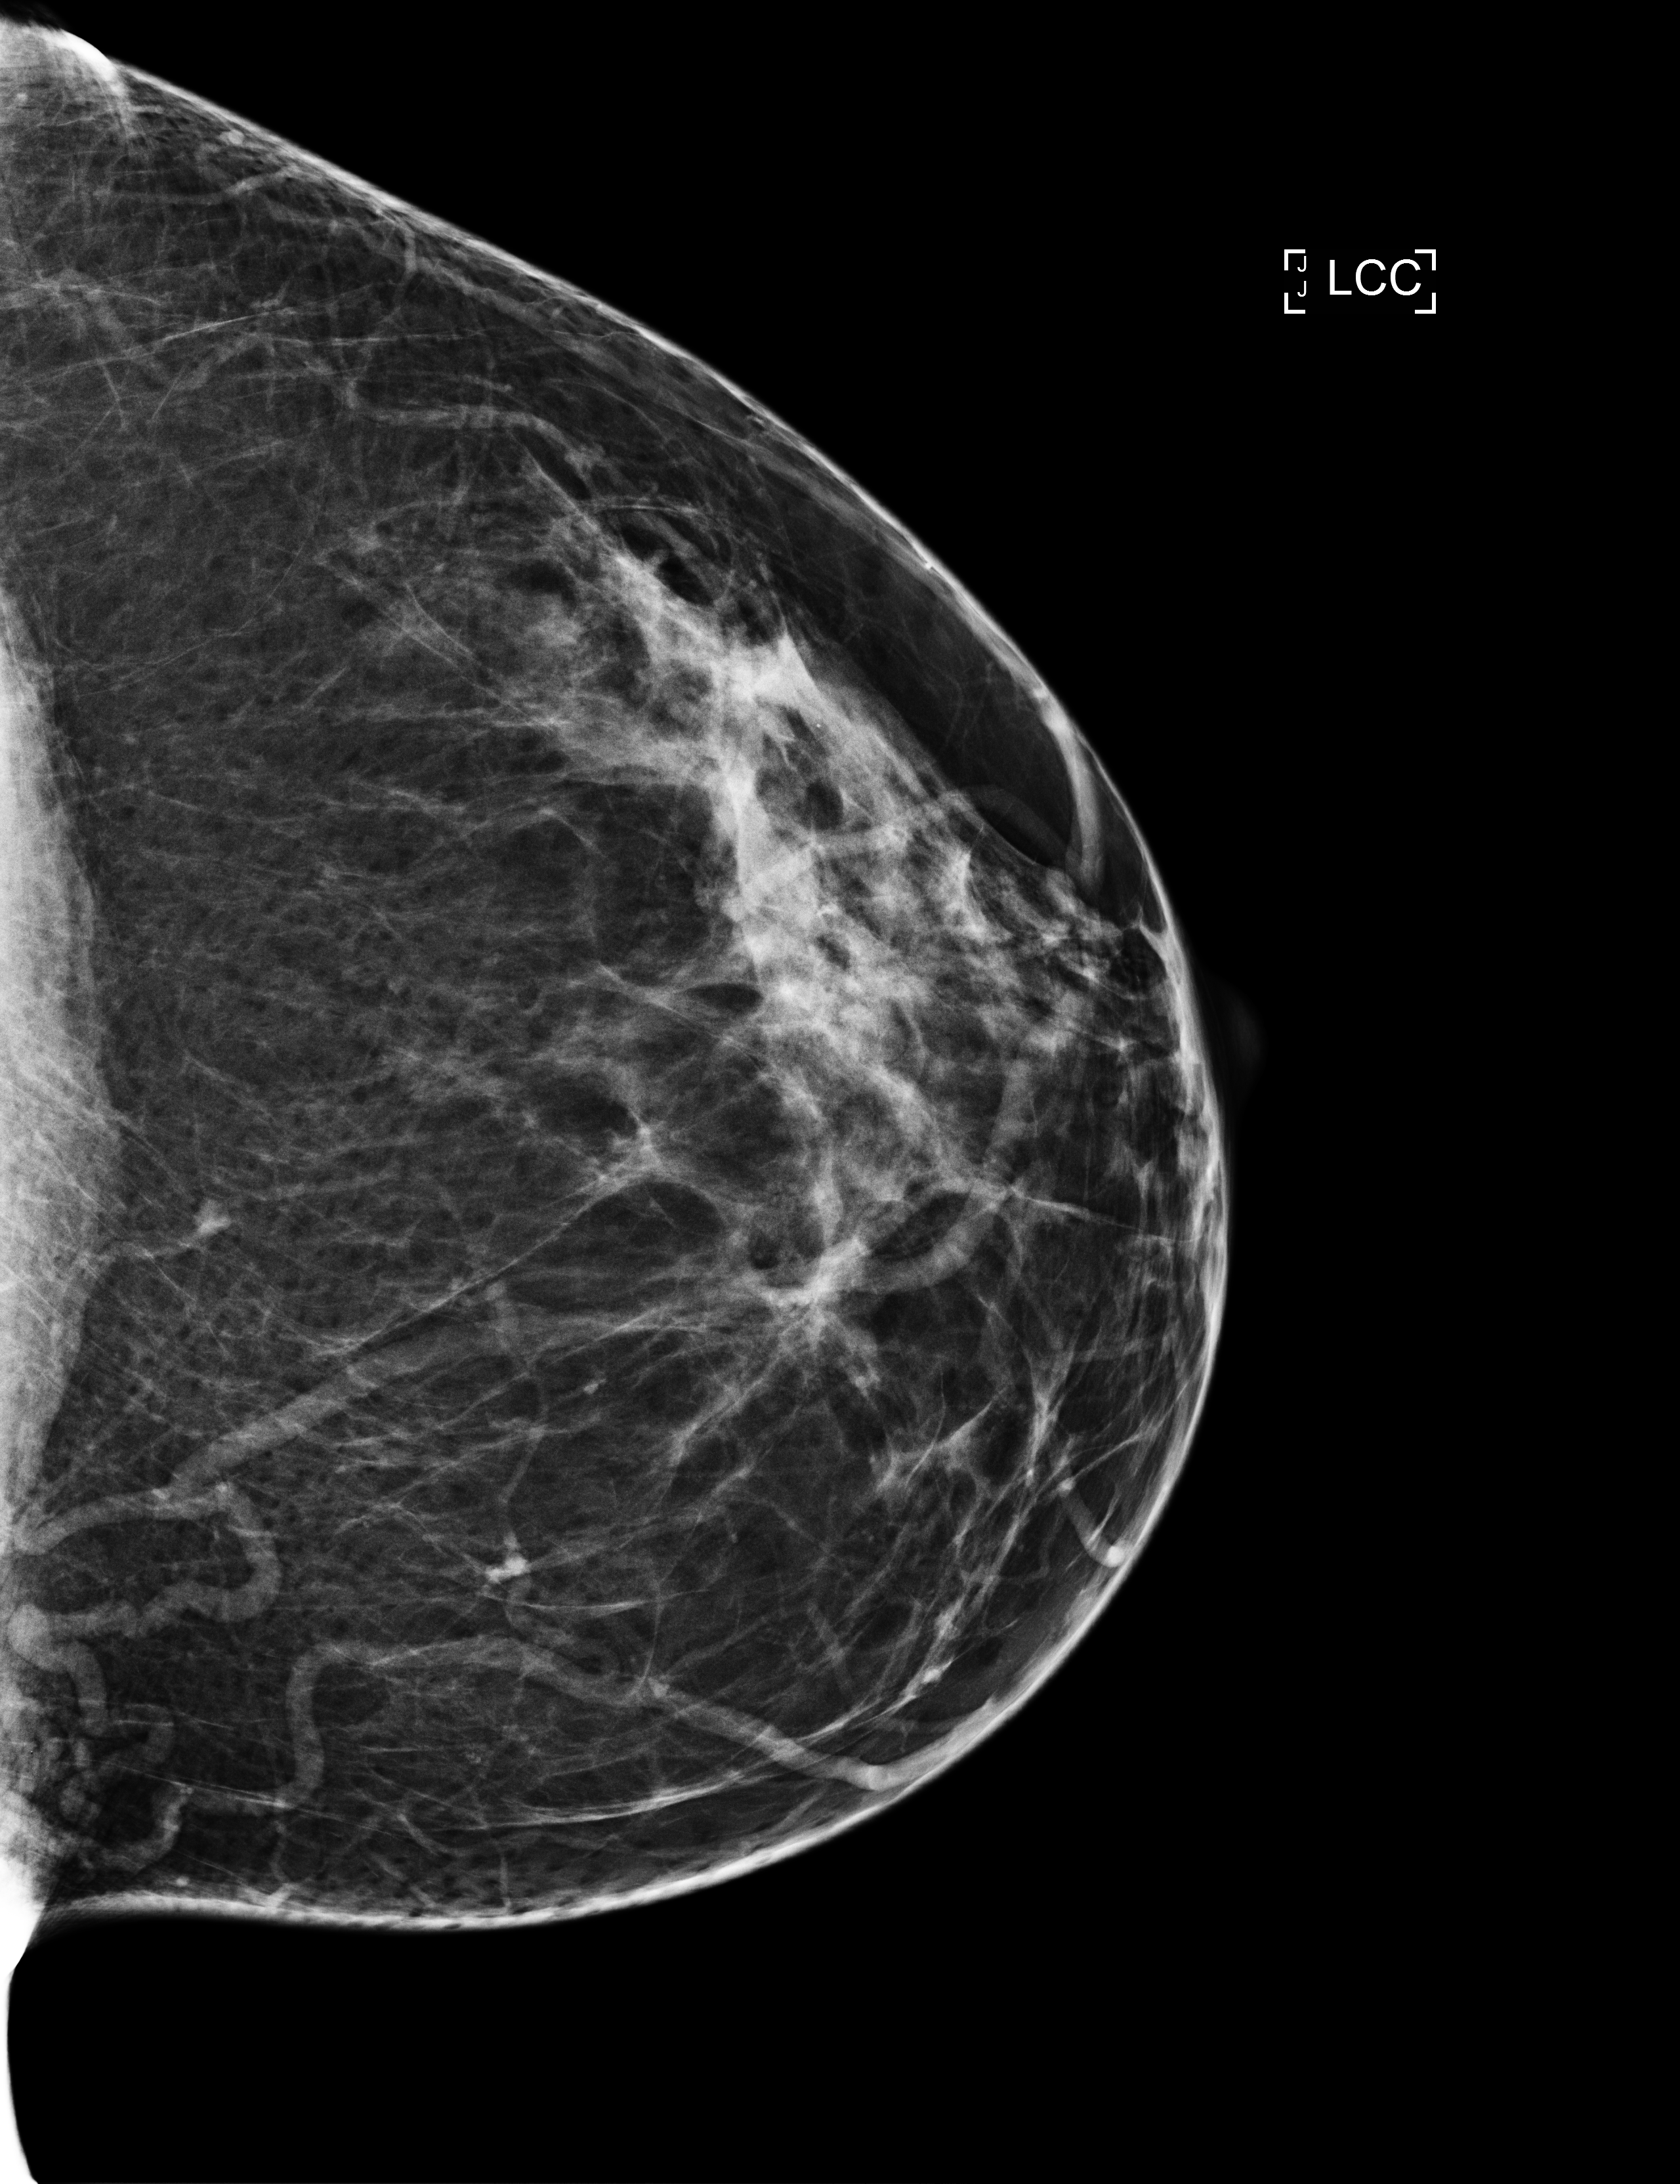
Digital mammogram (FFDM), left breast, cranio-caudal projection, screening examination. Patient: female, 41 years.
BI-RADS breast density category at the screening exam (both breasts, scale 1–4): 2. Final BI-RADS category for the screening round (tomosynthesis exam, both breasts): category 1. Recall: no recall after this screen.